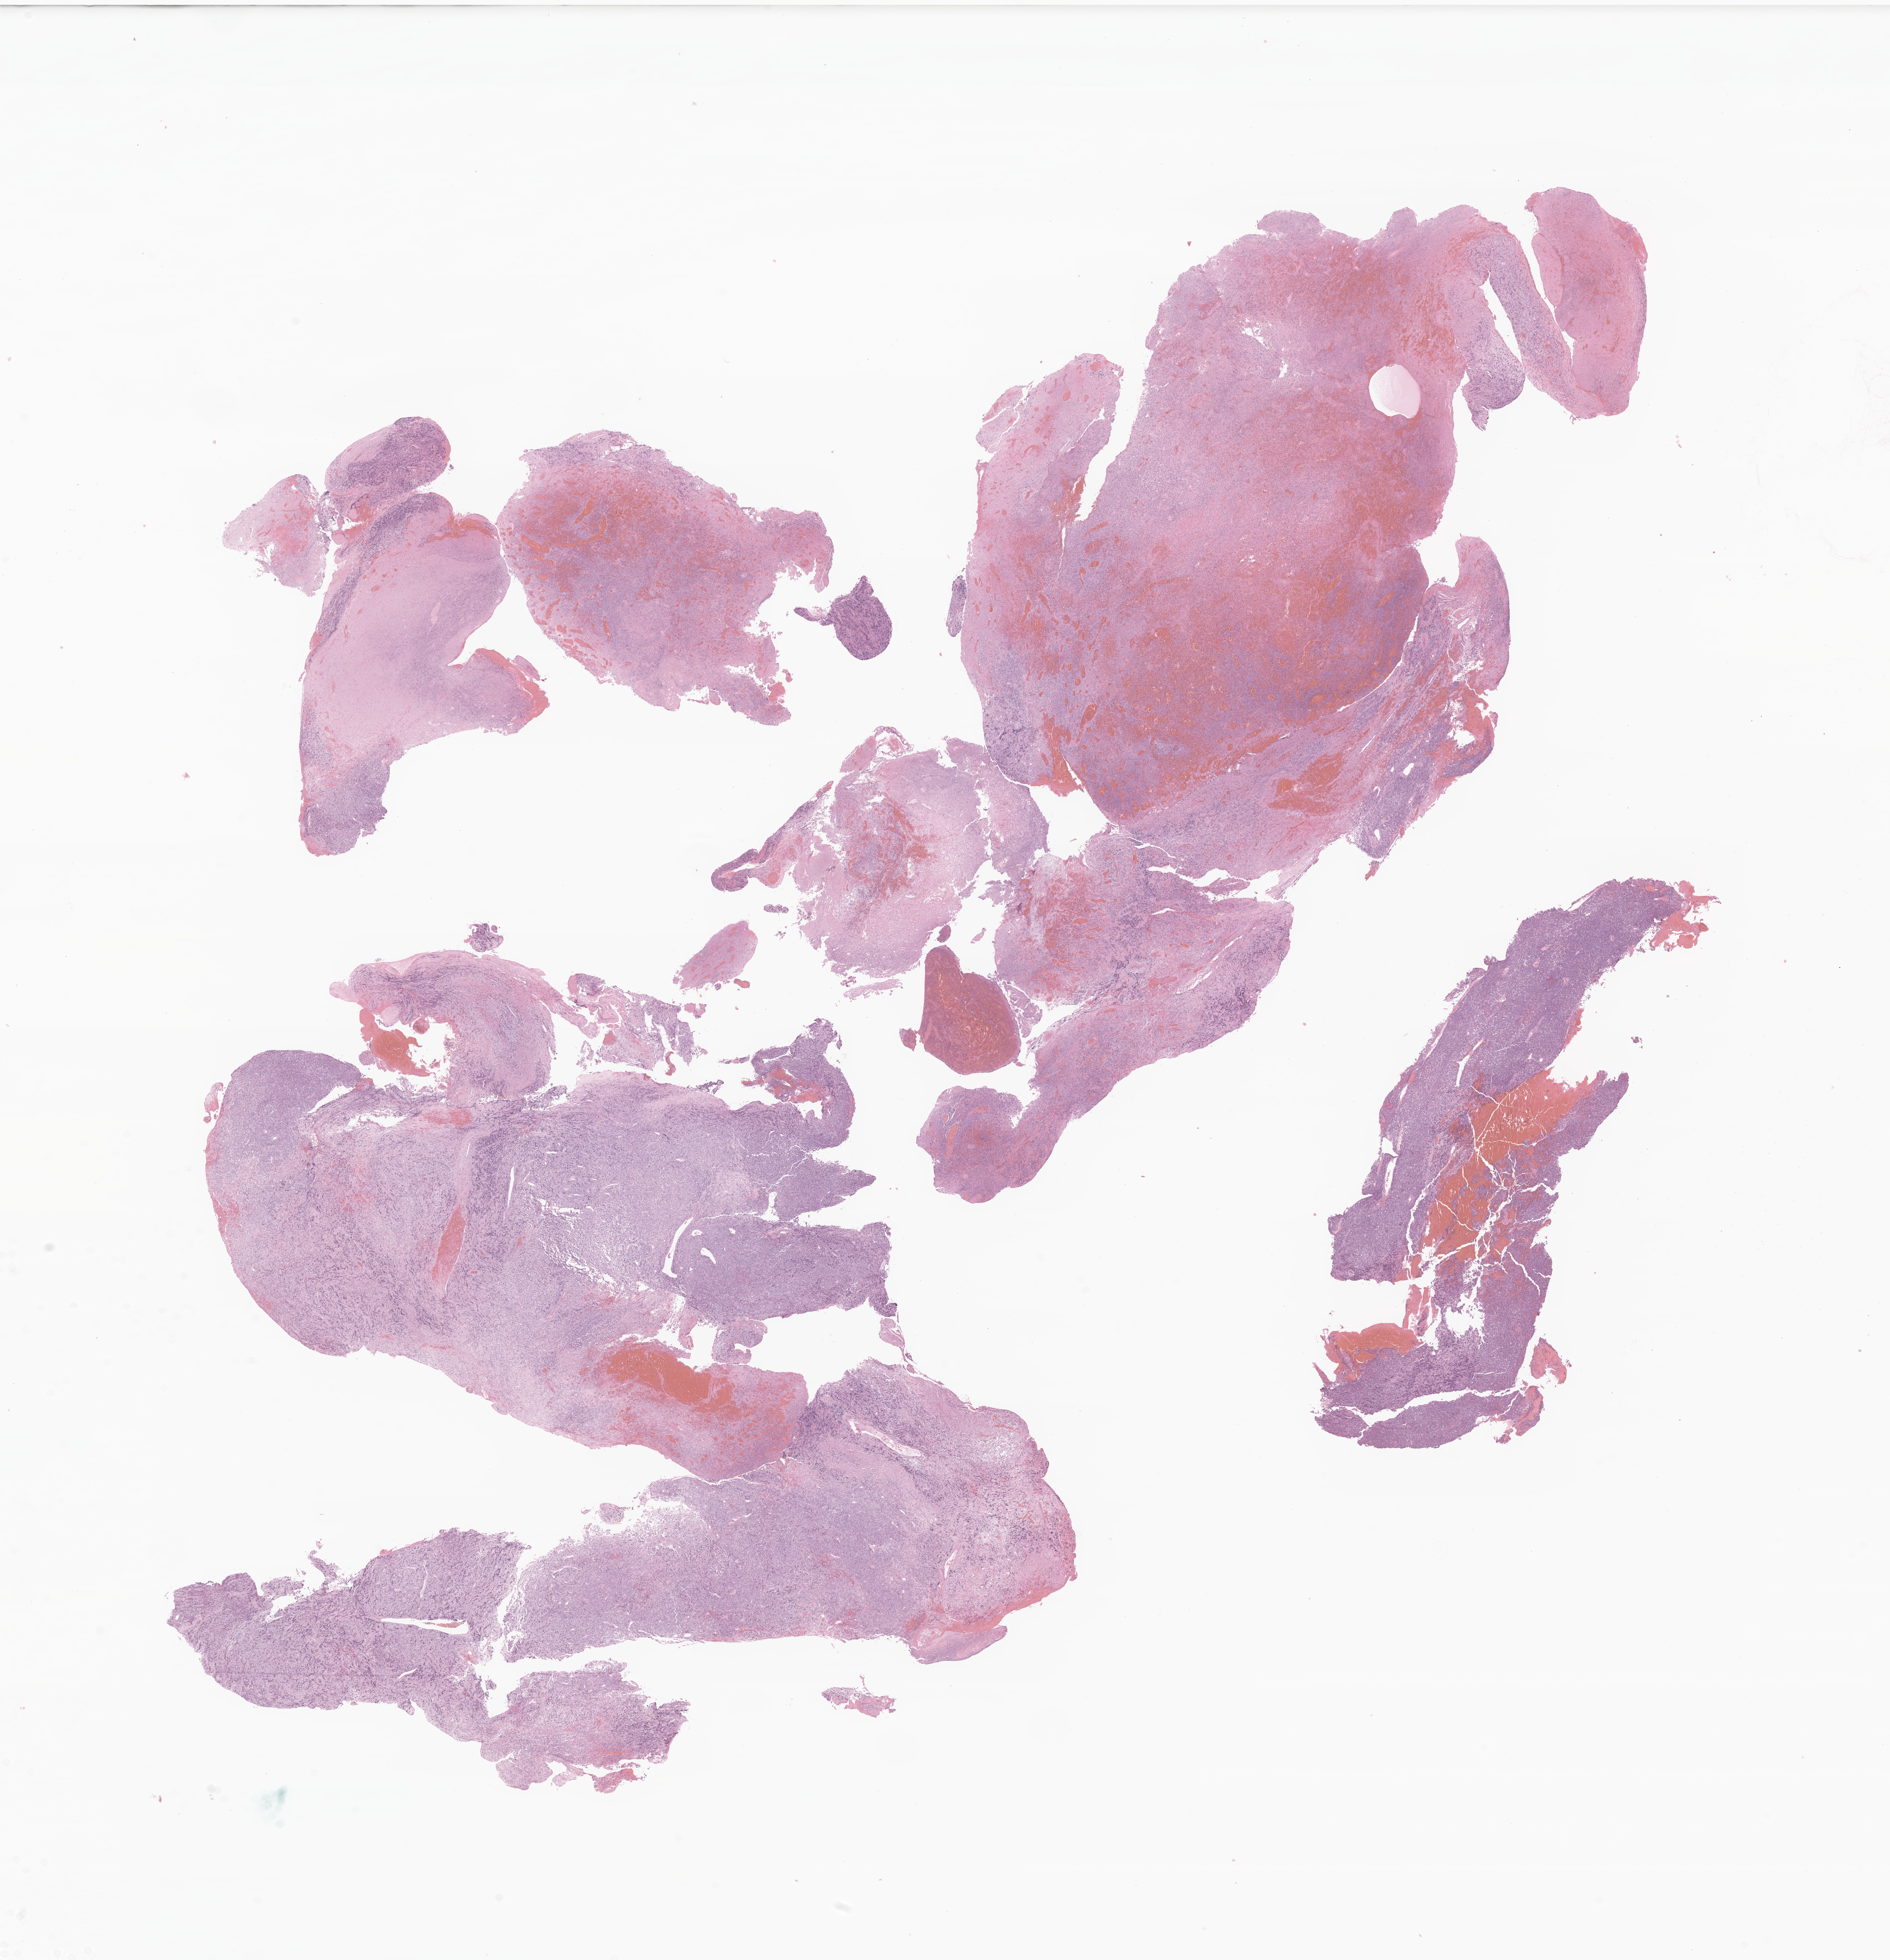
Whole-slide image, H&E stain of tumor tissue from the spinal cord, a low-resolution overview of the entire scanned area, about 21.3 x 22.1 mm. FFPE section. Patient: male, age 133 months (11 years 1 month).
• diagnosis (ICD-O-3 morphology term): Atypical teratoid/rhabdoid tumor